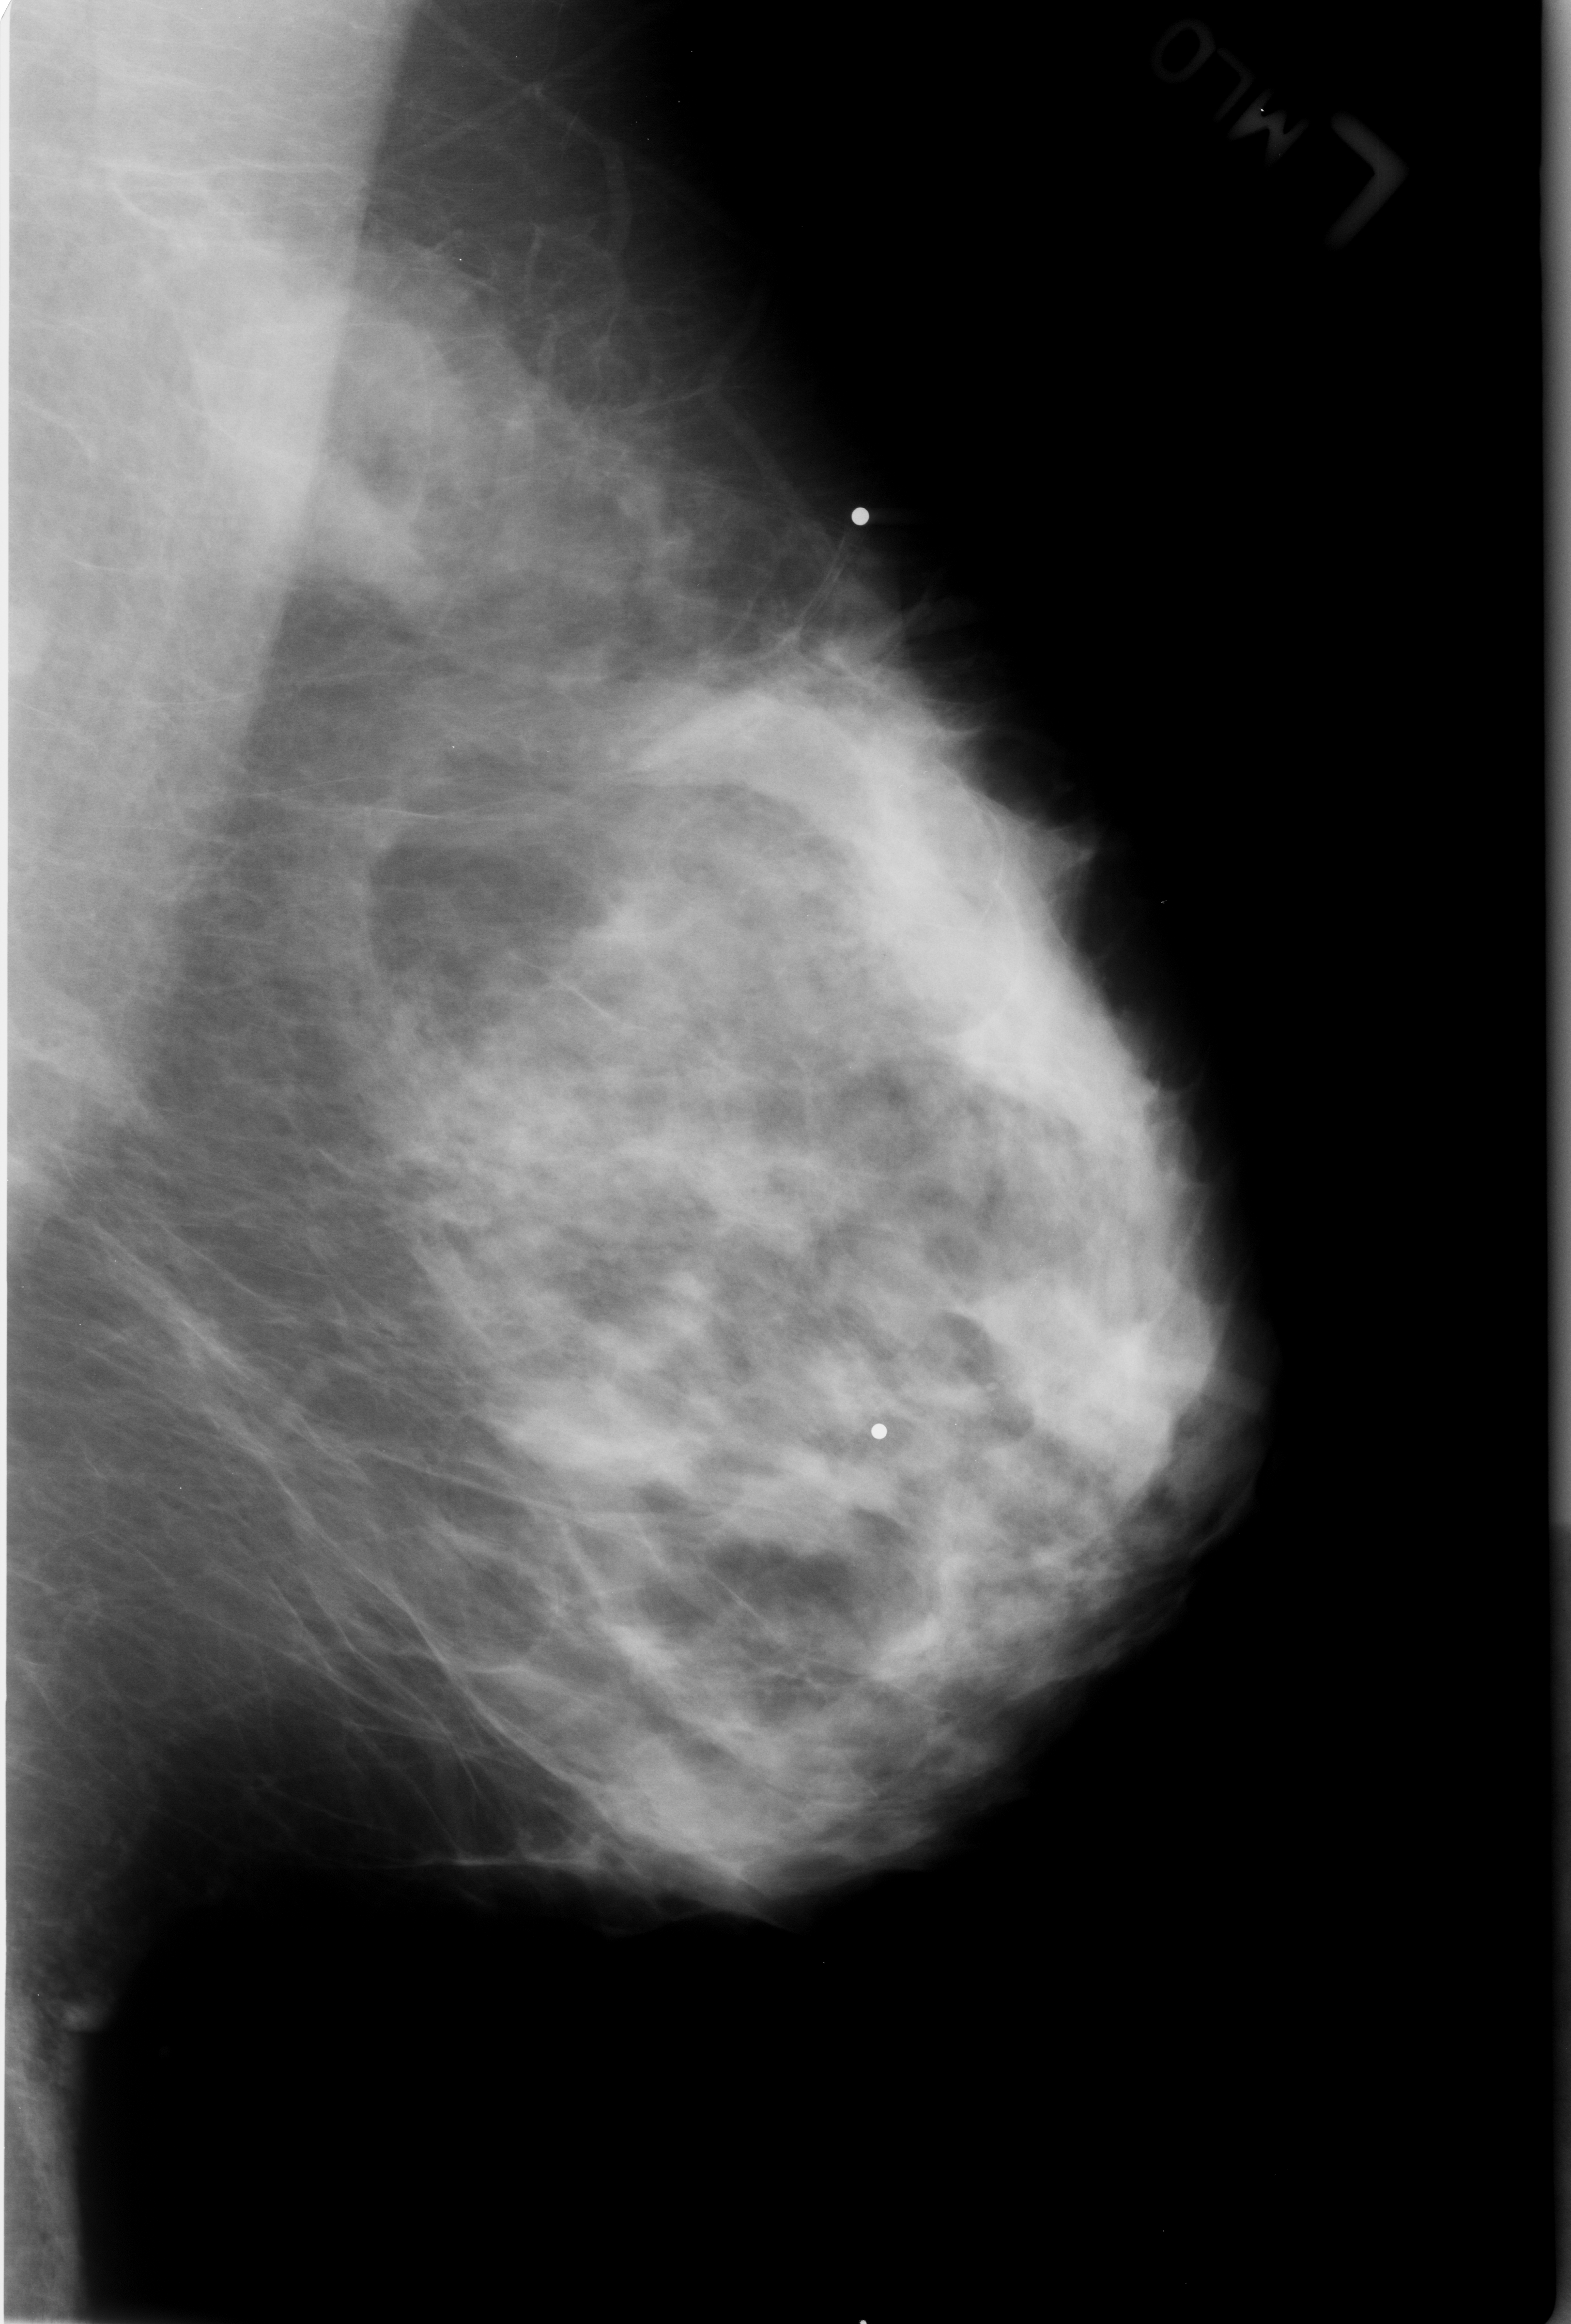
Scanned film-screen mammogram; left breast; mediolateral oblique (MLO) view; BI-RADS breast density category 3 (scale 1–4).
Abnormality record for this image: mass, shape focal asymmetric density; BI-RADS assessment category 2; subtlety rating 4 on a 1 (subtle) to 5 (obvious) scale; benign; no additional work-up was recommended (benign without callback).